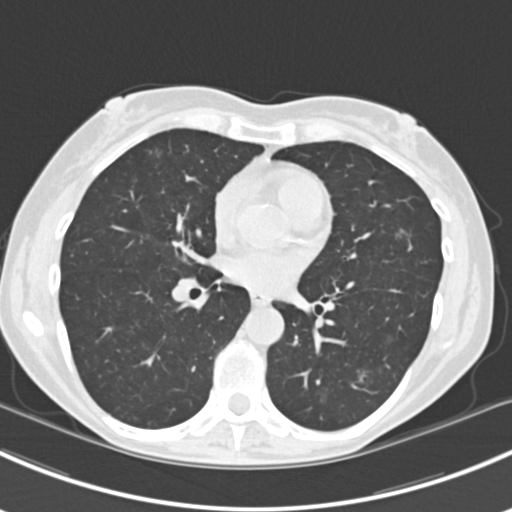
Axial slice from a low-dose chest CT screening exam, baseline screening round, lung window (W 1500 / L -600 HU), slice 97 of 224 in the series, 512 × 512 image matrix, field of view 310 × 310 mm. Female, age 63 years at enrolment.
• Expert reader's lesion annotation, bounding box <381,217,423,255> (left, top, right, bottom; pixels).
• The screening reader recorded 10 non-calcified nodules or masses ≥4 mm on this exam (right lower lobe, right lower lobe, left lower lobe, left lower lobe, right middle lobe, right lower lobe, left lower lobe, left upper lobe, right upper lobe, left upper lobe); which of them this box marks is not recorded.
• Lung cancer was diagnosed 751 days after this screen (after the third annual screen): bronchiolo-alveolar adenocarcinoma, NOS, right upper lobe, right middle lobe, right lower lobe, left upper lobe, left lower lobe, moderately differentiated (G2), stage IV (AJCC 6th edition).